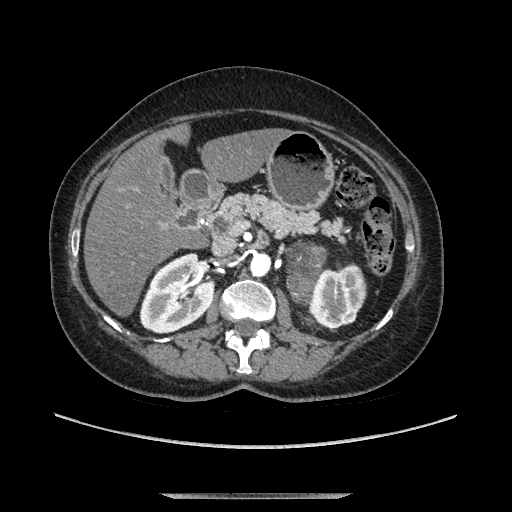
Contrast-enhanced abdominal CT, one axial slice. Slice 58 of 169 in the series (ordered by position). Soft-tissue window (W 400 / L 40 HU). 1.25 mm slice thickness. 512 × 512 image matrix, field of view 400 × 400 mm. Female patient. From the clinical record (not read from this slice): diagnosis: adrenocortical carcinoma; tumour side: left adrenal; tumour size at pathology: 9 cm; Ki-67 index: 2 %; stage (as recorded): 3.
Annotated regions visible in this slice (semi-automatic segmentation, software-assisted and operator-edited):
- mass: bounding box <287,242,324,305> (left, top, right, bottom; pixels)